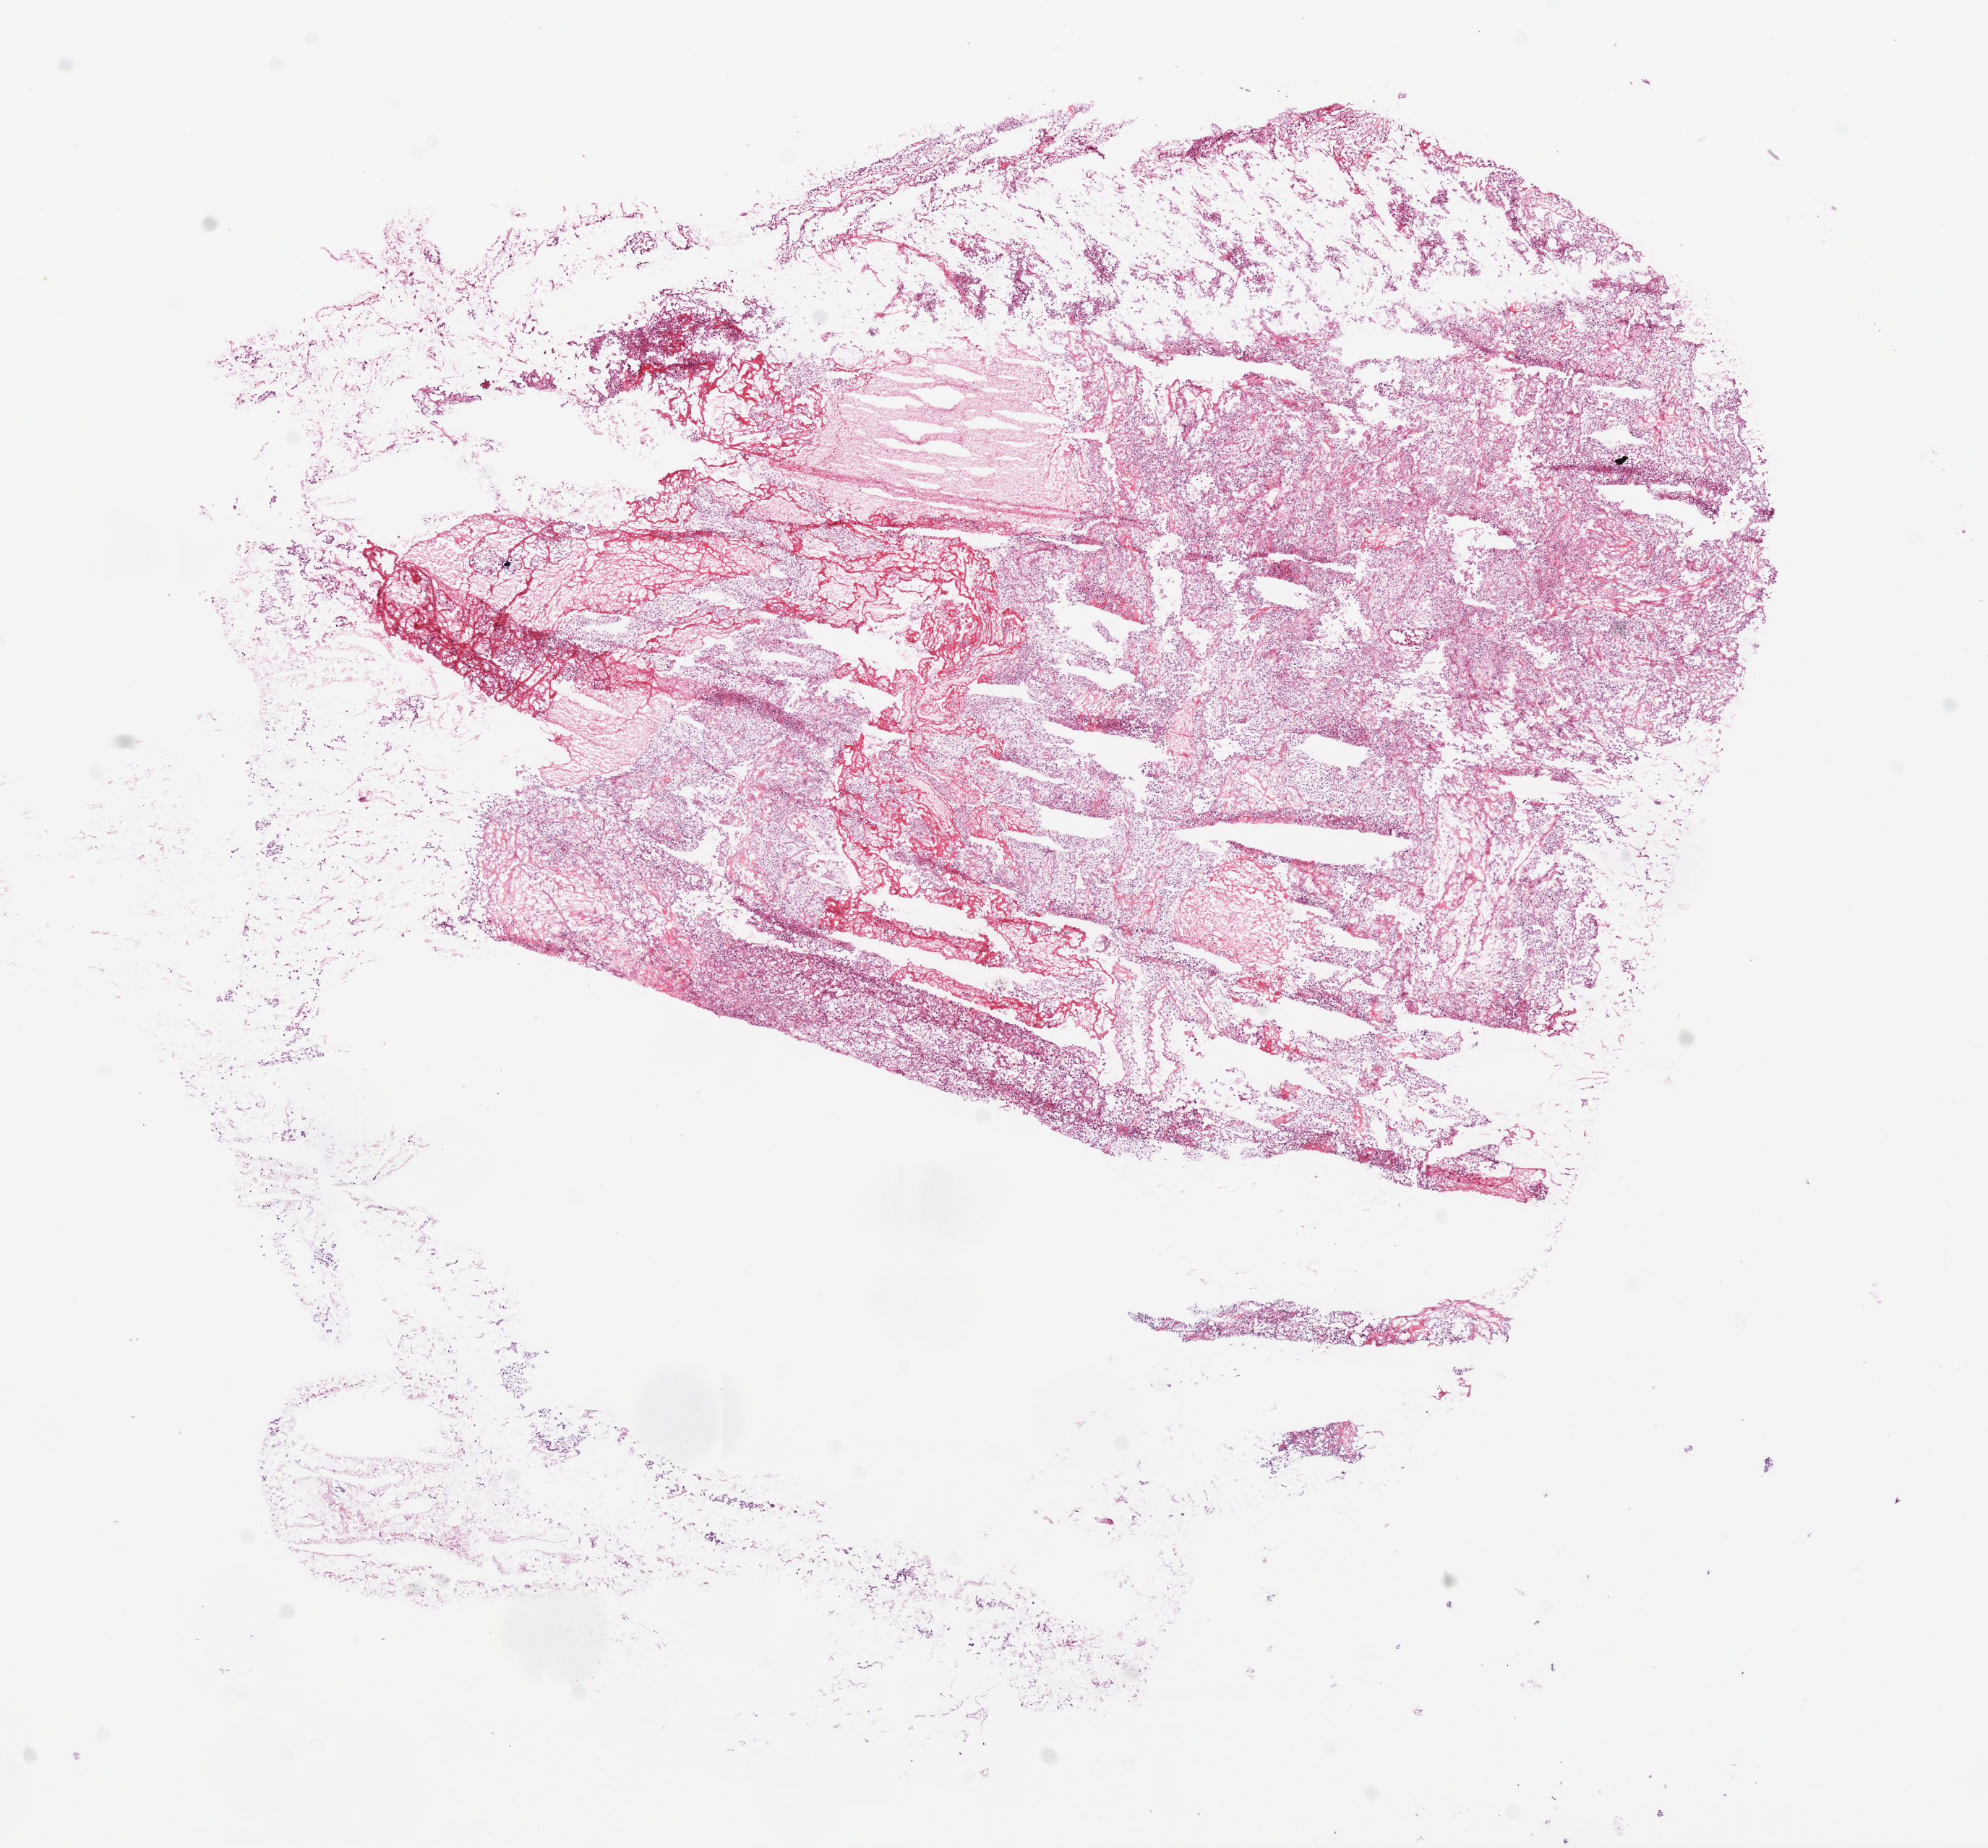
Whole-slide histology image, H&E, shown as a low-resolution overview of the whole scanned area (about 11.0 x 10.3 mm, acquisition: 20x scan). Frozen section. Kidney, primary tumour sample. Female patient; age at initial diagnosis 70 years. Histologic grade: G2 (moderately differentiated). Composition of this section per pathologist review: tumour cells 85%, tumour nuclei 85%, normal cells 0%, stromal cells 15%, necrosis 0%.
Laterality: left. Lymph nodes positive (case pathology): 0 of 2 examined. Histologic diagnosis: Clear cell adenocarcinoma, NOS. TNM: T3a N0 M0. AJCC pathologic stage: III (7th edition).